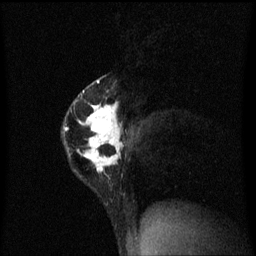
Breast MRI (dynamic contrast-enhanced), one sagittal slice; slice 41 of 60 in the series (ordered by position); dynamic contrast-enhanced series, image 2 of 3 at this slice position (ordered by acquisition); 1.5 T; TE 4.2 ms, TR 8.4 ms; 2 mm slice thickness; 256 × 256 image matrix, field of view 200 × 200 mm. Patient: female, 40 years.
Outlined on this slice (semi-automatic segmentation, software-assisted and operator-edited):
- analysis volume of interest (the breast-tissue region the enhancement analysis was run in; not a lesion): box from (x=63, y=74) to (x=125, y=183) px
- tumour enhancement mask (voxels above the 70 % enhancement threshold inside the analysis volume of interest): (x=64, y=80)–(x=125, y=173)